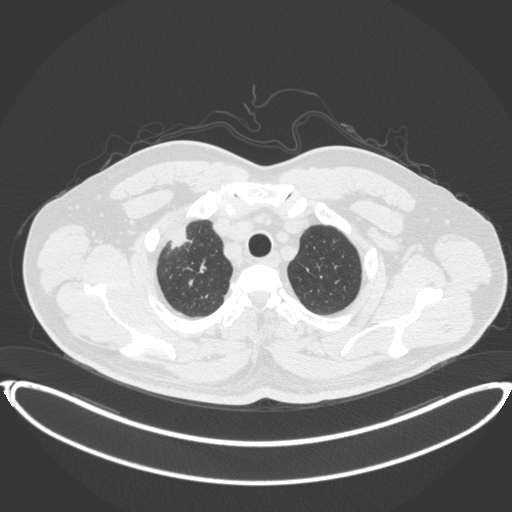
Chest CT, one axial slice. Position 342 of 399 along the scan axis. 120 kVp. Lung window (W 1500 / L -600 HU). 1 mm slice thickness. 512 × 512 image matrix, field of view 445 × 445 mm. Patient: male, 53 years. Case-level facts recorded for this patient, not image findings: clinical TNM (as recorded): T2a N0 M0.
Annotated regions visible in this slice (rectangle marked by the reading radiologist):
- lung tumour (recorded histology: adenocarcinoma): bounding box [x1, y1, x2, y2] px = [165, 223, 198, 256]